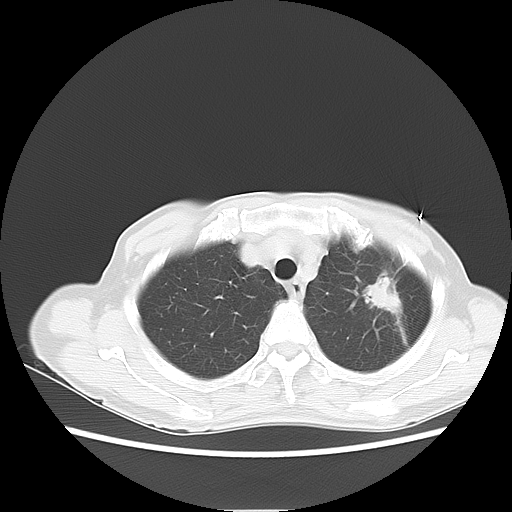
Chest CT, one axial slice. Position 10 of 14 along the scan axis. Reconstruction kernel LUNG. Lung window (W 1500 / L -600 HU). 512 × 512 image matrix. Patient: female, 71 years. Case-level facts recorded for this patient, not image findings: clinical TNM (as recorded): T2 N0 M0.
Structures marked on this image (bounding box drawn by a radiologist):
- lung tumour (recorded histology: adenocarcinoma): bounding box <360,269,408,318> (left, top, right, bottom; pixels)